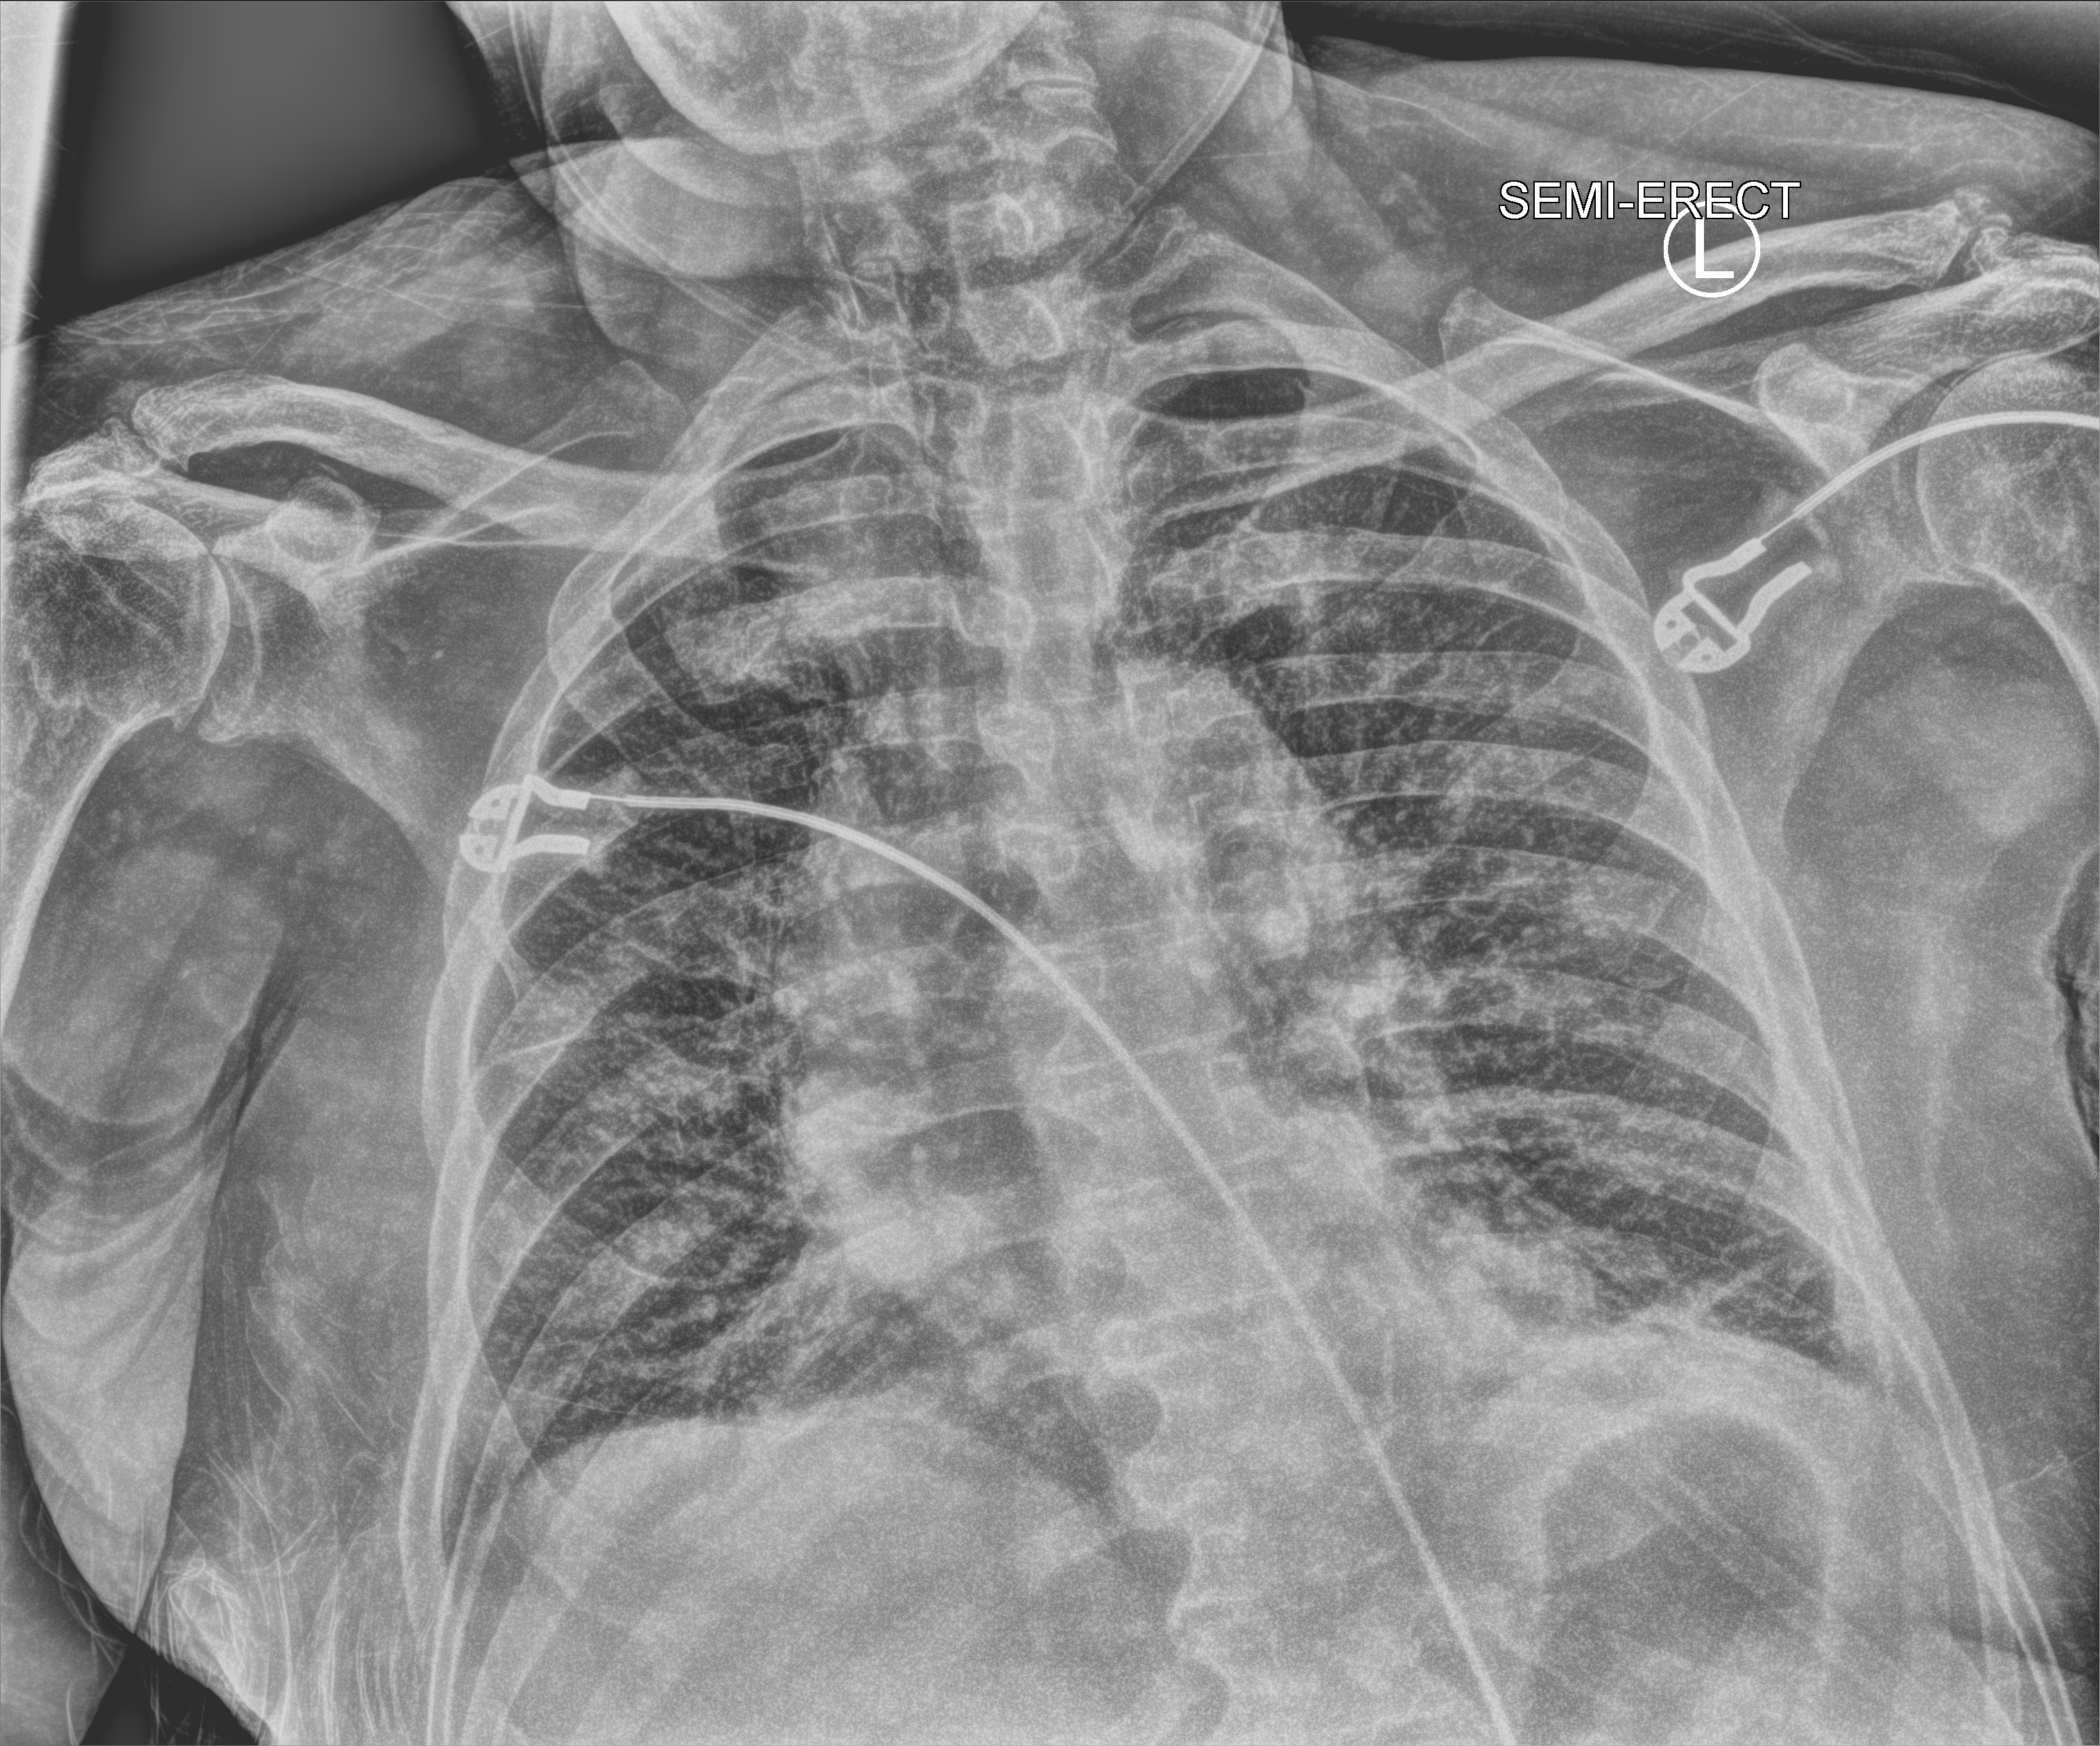
Bedside chest radiograph (computed radiography), anteroposterior (AP) projection. Male patient hospitalised with COVID-19, age 75–90 years.
Hospital-stay facts (about this admission, not read from this image; timing relative to this image not recorded):
- mechanically ventilated during this hospital stay: no